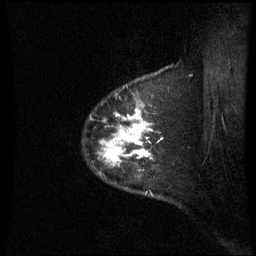
Breast MRI (dynamic contrast-enhanced), one sagittal slice. Position 53 of 60 along the scan axis. Dynamic contrast-enhanced series, image 2 of 3 at this slice position (ordered by acquisition). 1.5 T. TE 4.2 ms, TR 8.9 ms. 2.4 mm slice thickness. 256 × 256 image matrix. Female patient, age 42 years. Case-level facts recorded for this patient, not image findings: setting: breast cancer imaged before/during neoadjuvant chemotherapy; receptor status: HER2-positive.
Outlined on this slice (semi-automatic segmentation, software-assisted and operator-edited):
- analysis volume of interest (the breast-tissue region the enhancement analysis was run in; not a lesion): bounding box <92,94,164,193> (left, top, right, bottom; pixels)
- tumour enhancement mask (voxels above the 70 % enhancement threshold inside the analysis volume of interest): <102,110,152,165>